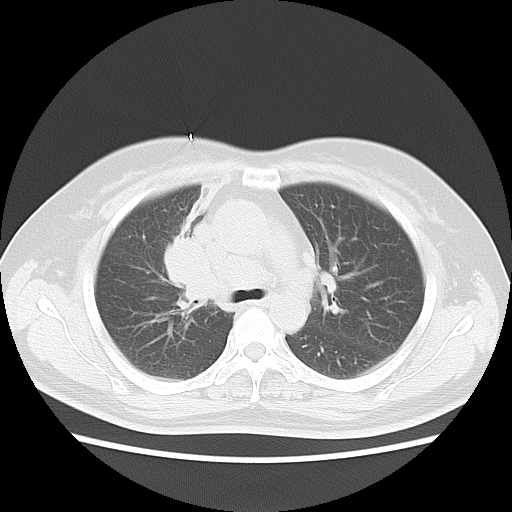
Chest CT, one axial slice. Position 8 of 18 along the scan axis. 120 kVp. Lung window (W 1500 / L -600 HU). 512 × 512 image matrix. Patient: female, 54 years. Case-level facts recorded for this patient, not image findings: clinical TNM (as recorded): T2 N3 M0.
Structures marked on this image (rectangle marked by the reading radiologist):
- lung tumour (recorded histology: small cell carcinoma): bounding box (x1, y1, x2, y2) in pixels: (151, 228, 221, 317)